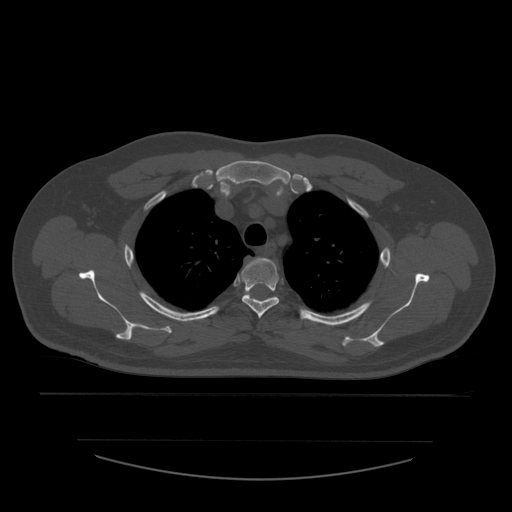
CT including the spine, one axial slice. Slice 434 of 532 in the series (ordered by position). Bone window (W 1800 / L 400 HU). 1.25 mm slice thickness. 512 × 512 image matrix, field of view 441 × 441 mm. Patient age 44 years. From the clinical record (not read from this slice): primary cancer: soft tissue sarcoma.
Annotated regions visible in this slice (semi-automatically segmented with operator editing):
- T3 vertebra: bounding box (x1, y1, x2, y2) in pixels: (241, 258, 280, 319)
- T4 vertebra: (248, 291, 250, 296)